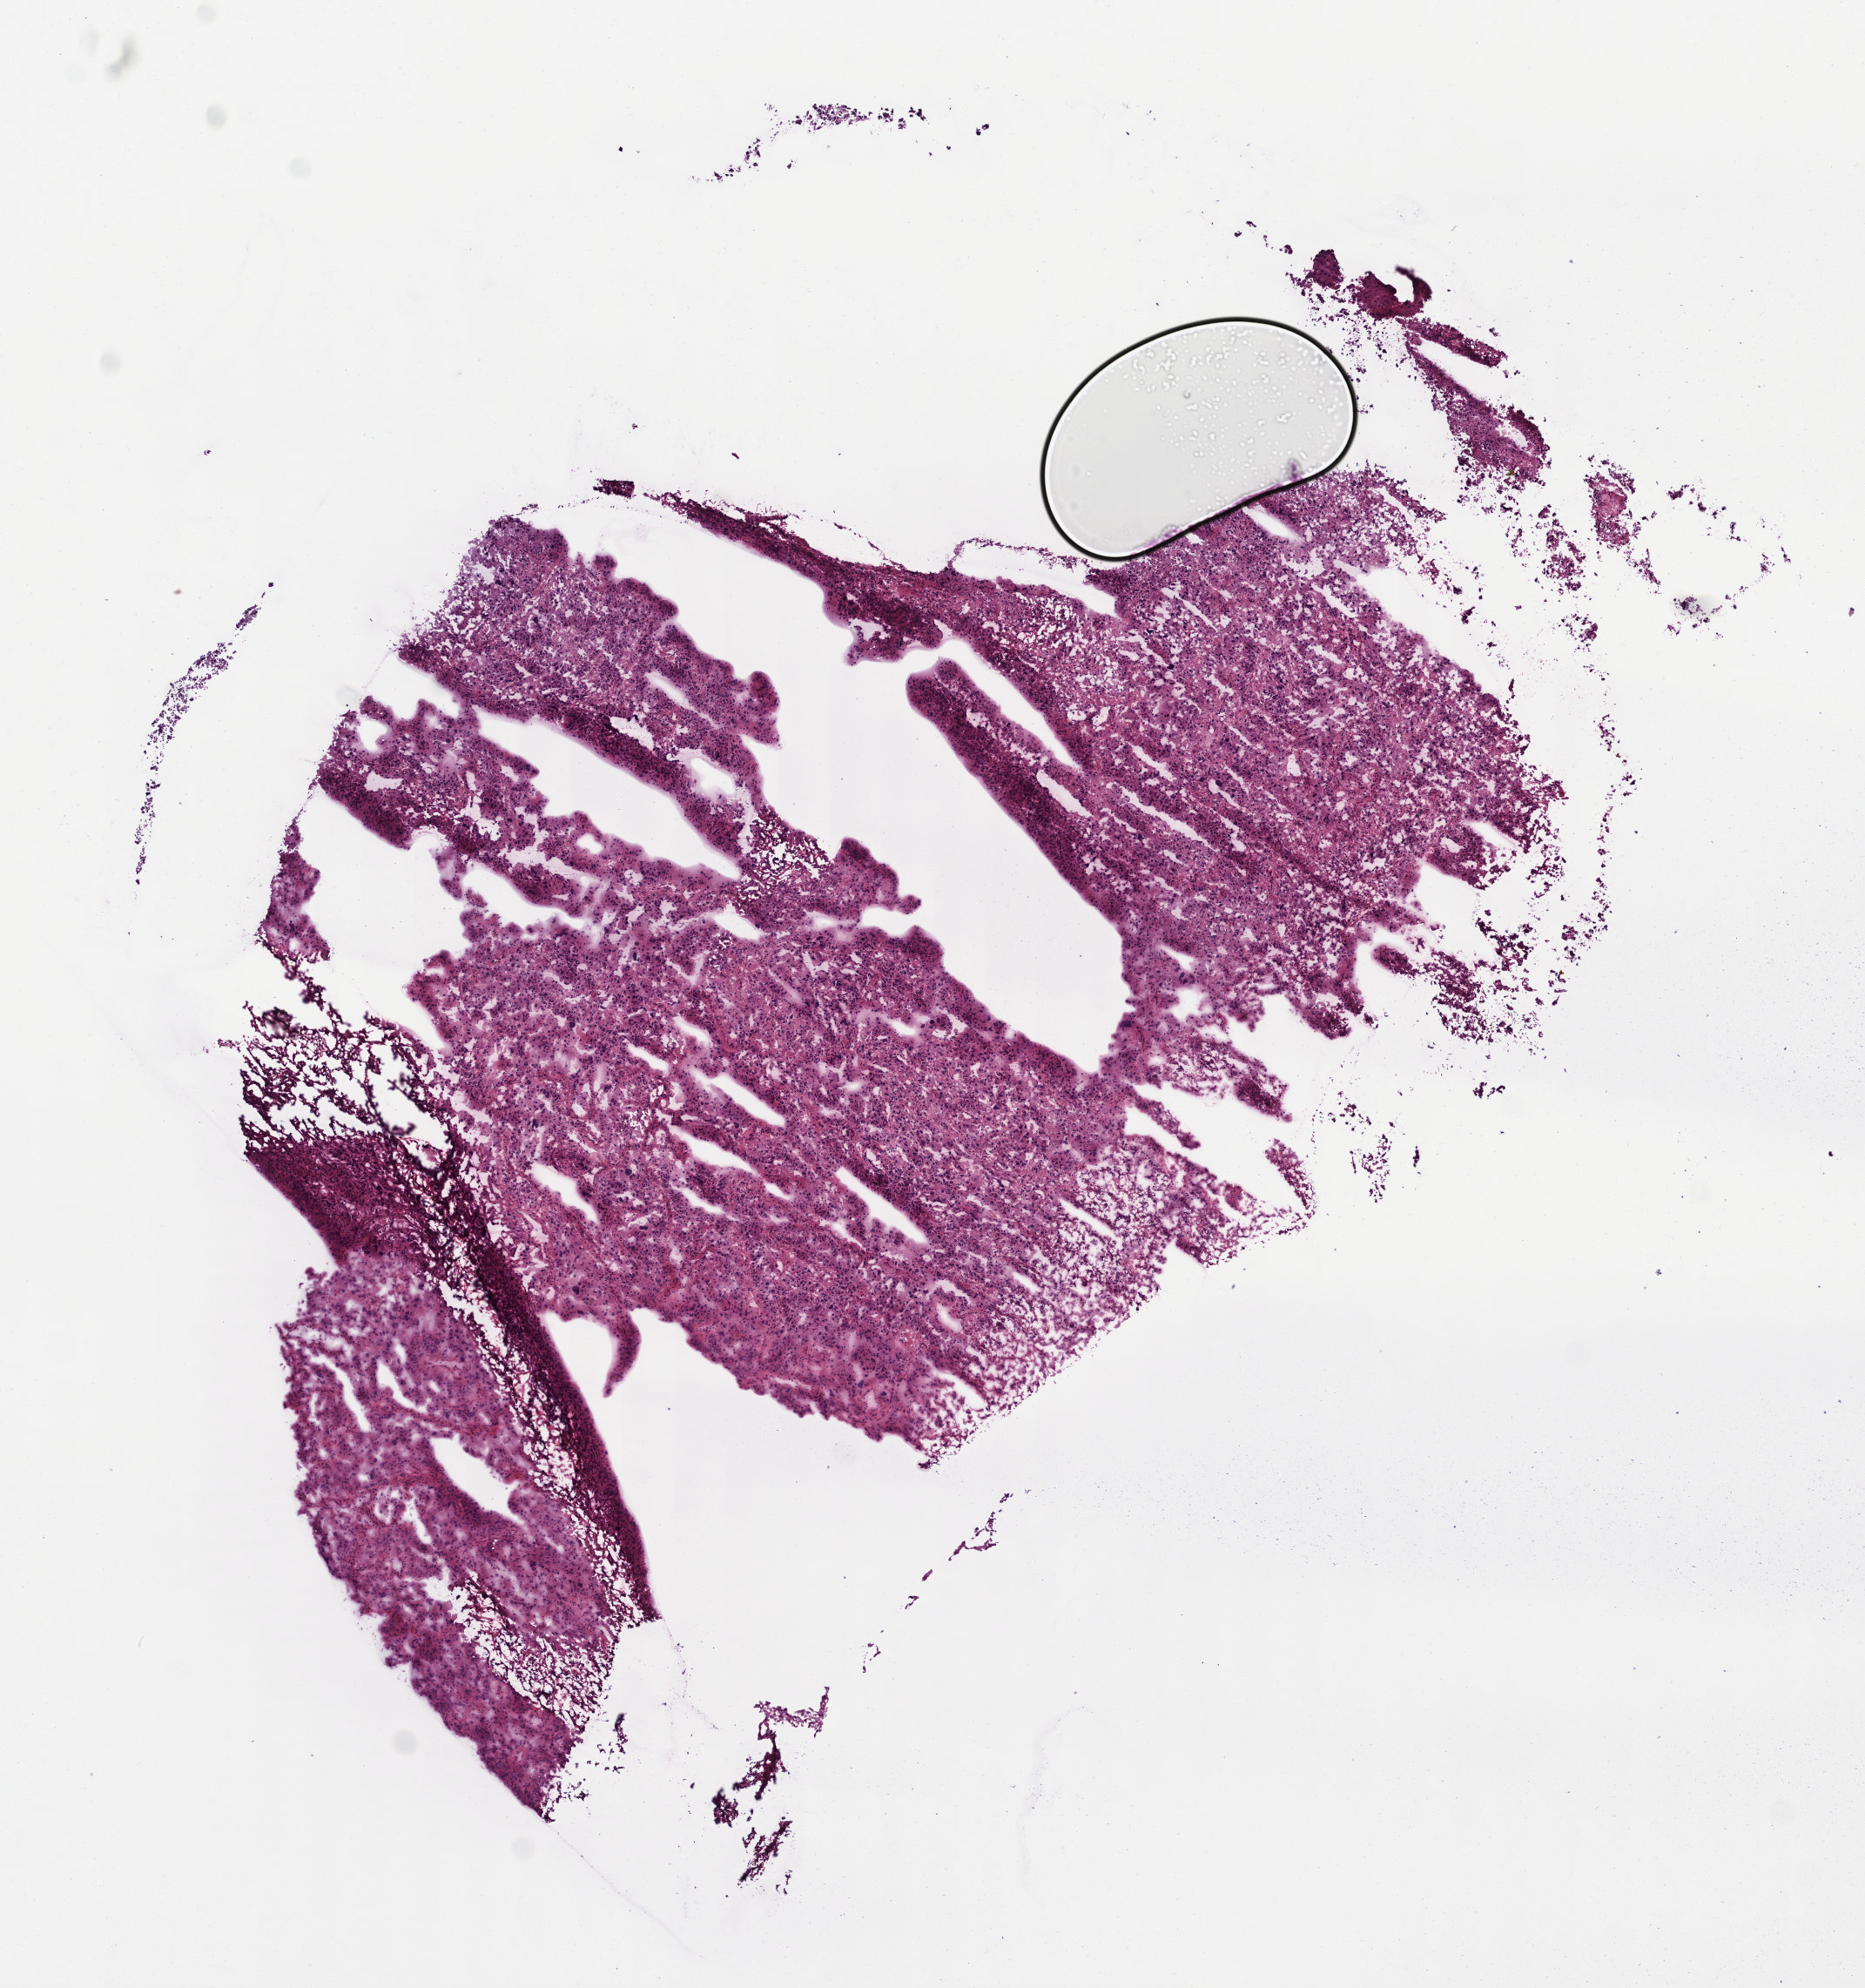
Digitized H&E tissue section (whole slide) — whole scanned area (about 8.4 x 9.0 mm, from a 40x scan) shown as a low-resolution overview. Frozen section from the top of the tissue portion. Adrenal gland, primary tumour sample. Patient: female, age at initial diagnosis 35 years. Pathologist review of this section (percent, as recorded): tumour cells 100%, tumour nuclei 95%.
Diagnosis: Pheochromocytoma, NOS.